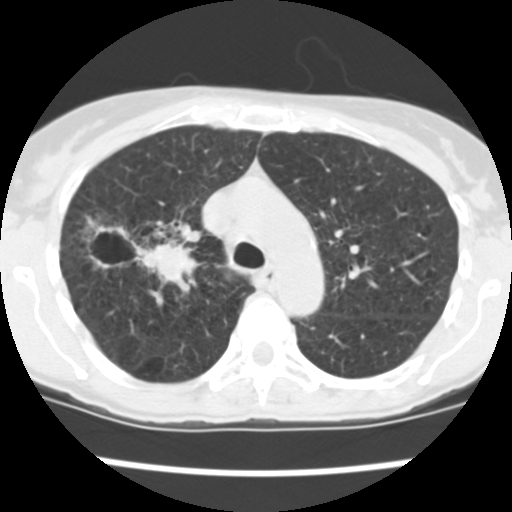
Axial slice from a low-dose chest CT screening exam. Baseline annual screen. Lung window (W 1500 / L -600 HU). 512 × 512 image matrix. Female, age 60 years at enrolment. Current smoker at enrolment.
- Expert reader's lesion annotation, bounding box (x1, y1, x2, y2) in pixels: (84, 216, 198, 285).
- The screening reader recorded 3 non-calcified nodules or masses ≥4 mm on this exam (right upper lobe, right upper lobe, right lower lobe); which of them this box marks is not recorded.
- Official screen result: positive, change unspecified: nodule(s) >= 4 mm or enlarging nodule(s), mass(es), or other non-specific abnormalities suspicious for lung cancer.
- Lung cancer was diagnosed 19 days after this screen: non-small cell carcinoma, right upper lobe, stage IV (AJCC 6th edition), 26 mm at pathology.